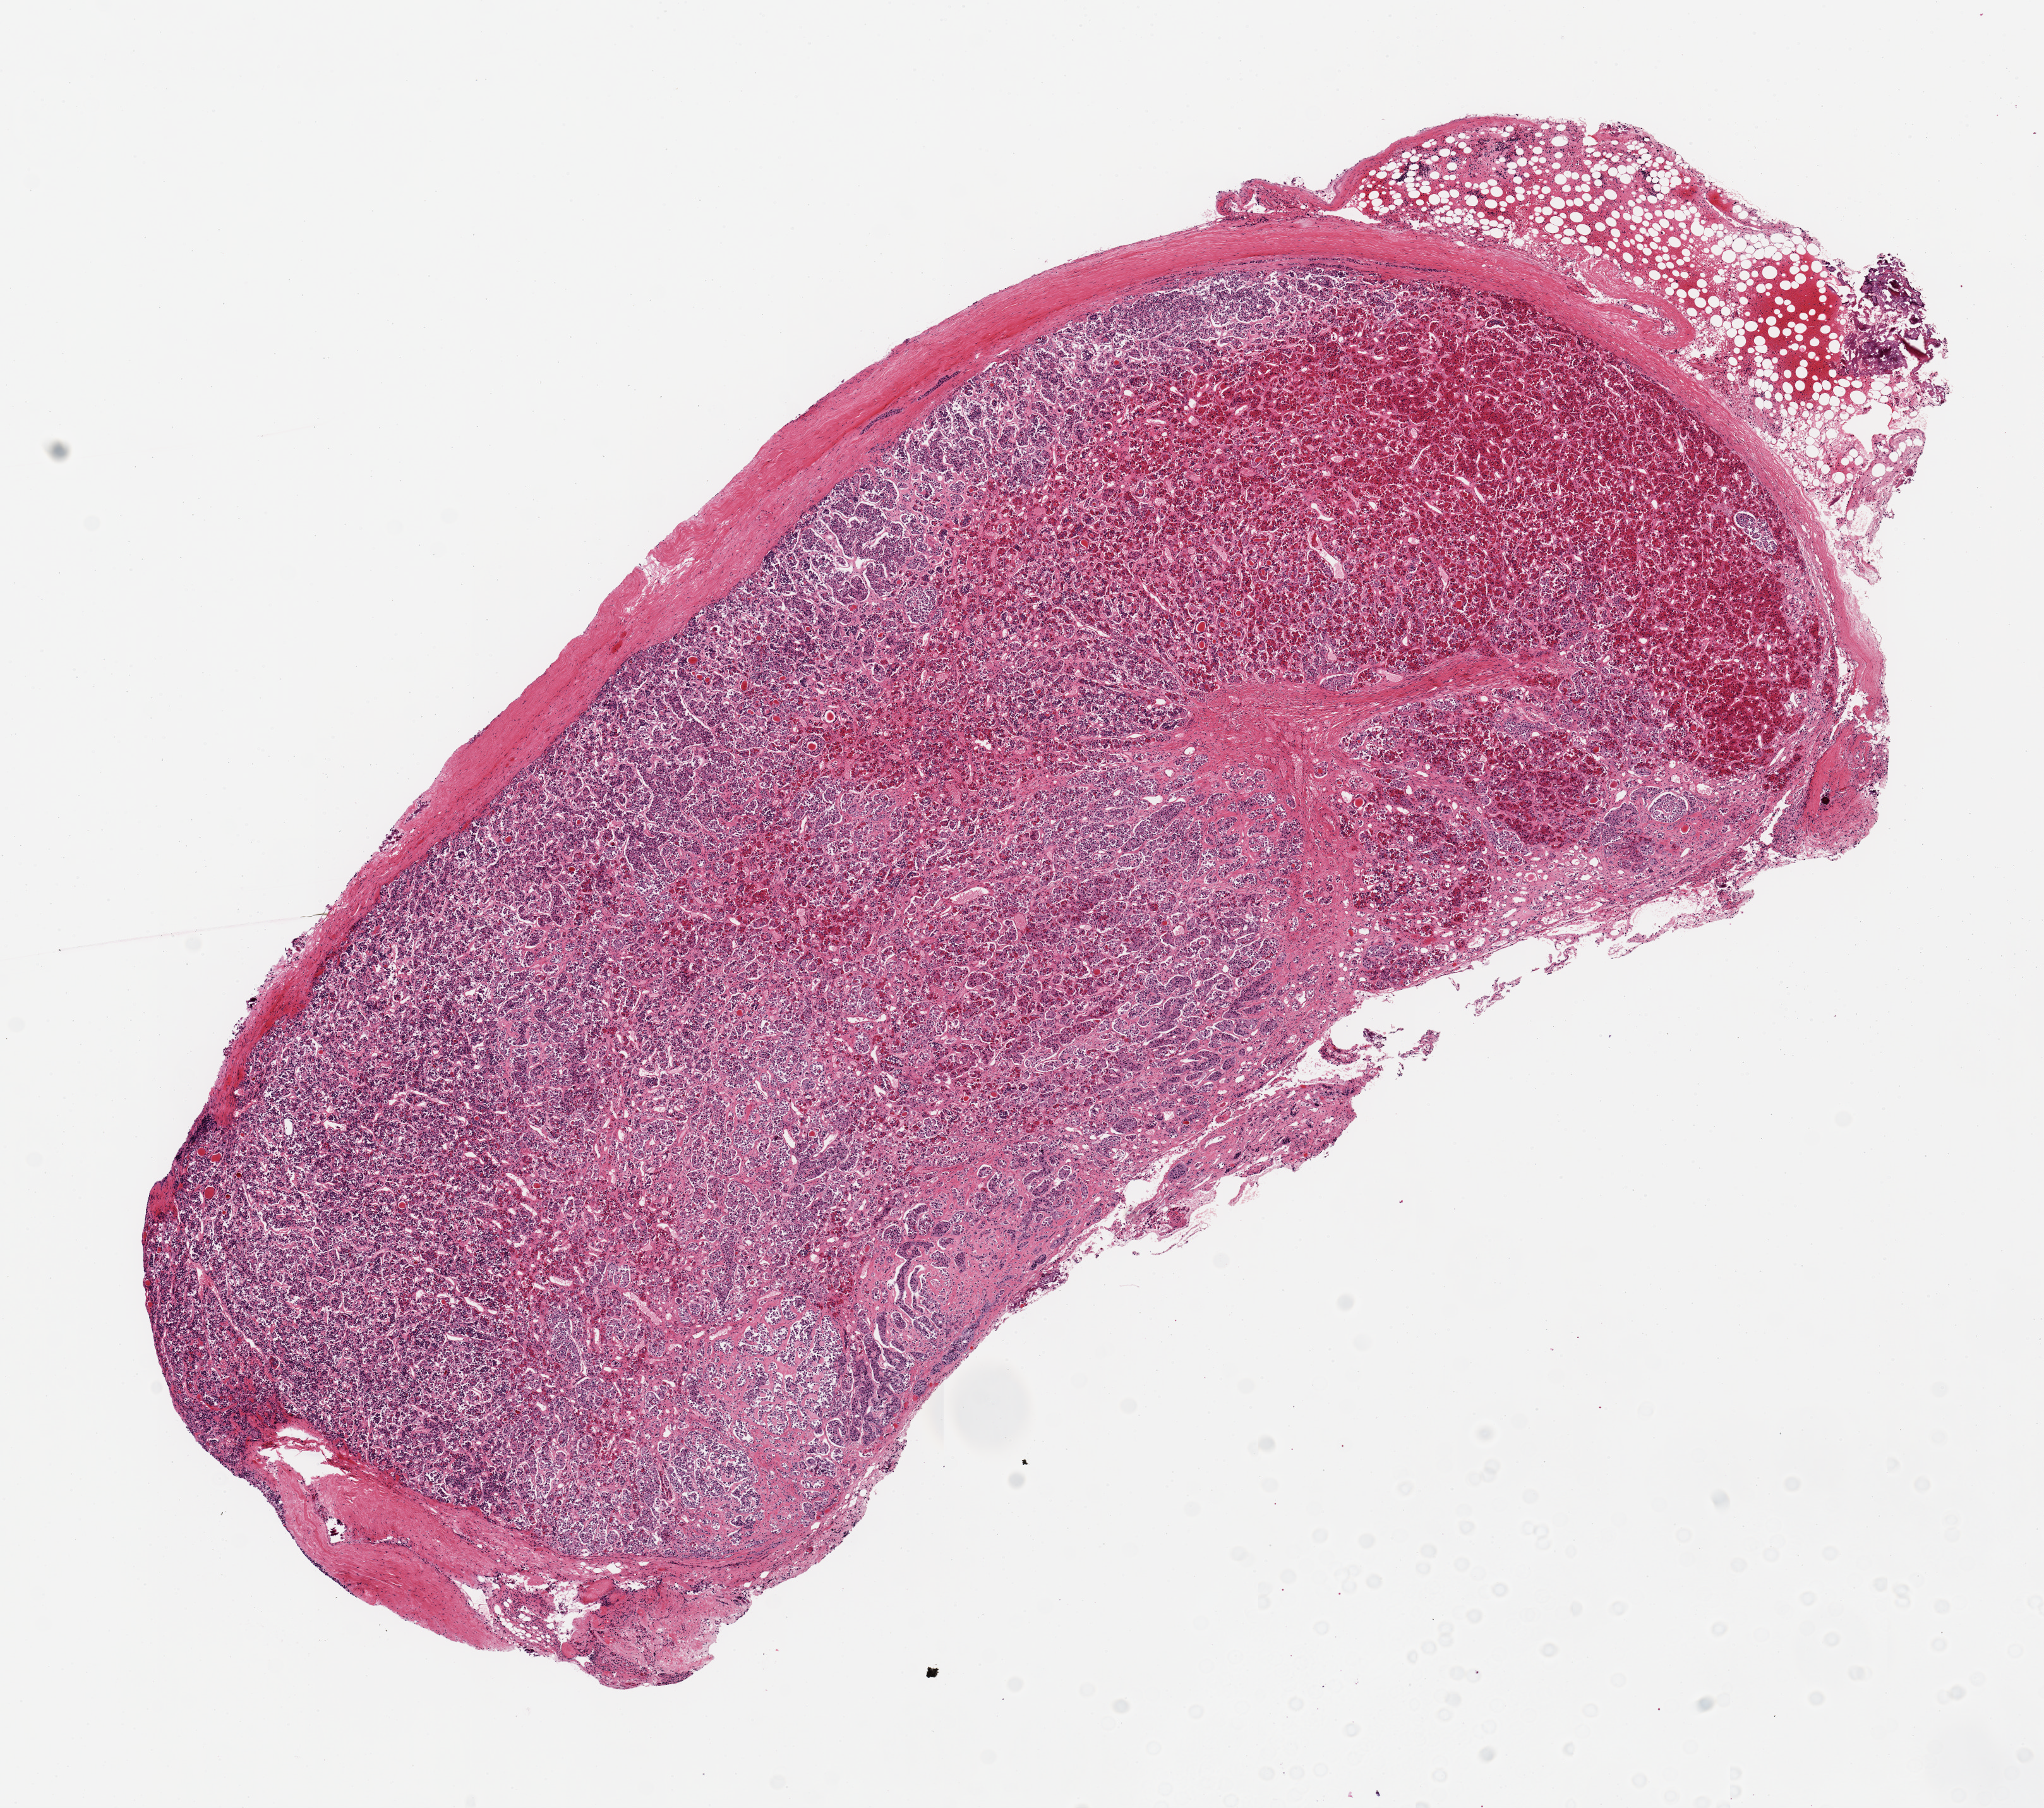
Digitized haematoxylin and eosin-stained section, brightfield — whole scanned area (about 12.8 x 11.3 mm, from a 20x scan) shown as a low-resolution overview; PAXgene-fixed paraffin-embedded (PFPE) section; sampled site (target tissue): pituitary; donor tissue sample. Female donor.
- review note (as recorded): 1 ~11x4.5mm aliquot